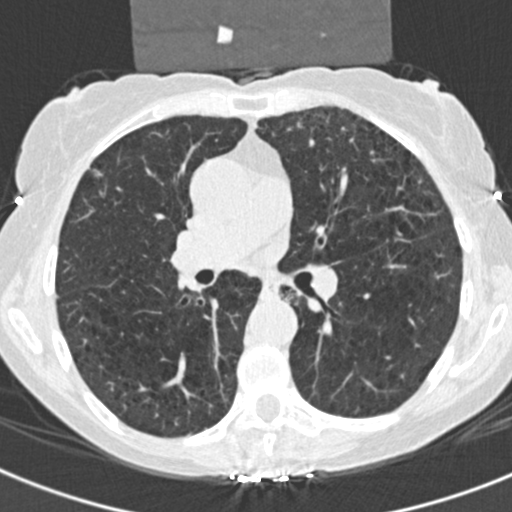
Low-dose screening chest CT, one axial slice; position 110 of 181 along the scan axis; reconstruction kernel B30f; lung window (W 1500 / L -600 HU); 2 mm slice thickness; 512 × 512 image matrix, field of view 298 × 298 mm.
Structures marked on this image (outlined manually by an expert reader):
- lesion 1 (tumor, upper lobe of right lung): bounding box (x1, y1, x2, y2) in pixels: (91, 169, 104, 176)